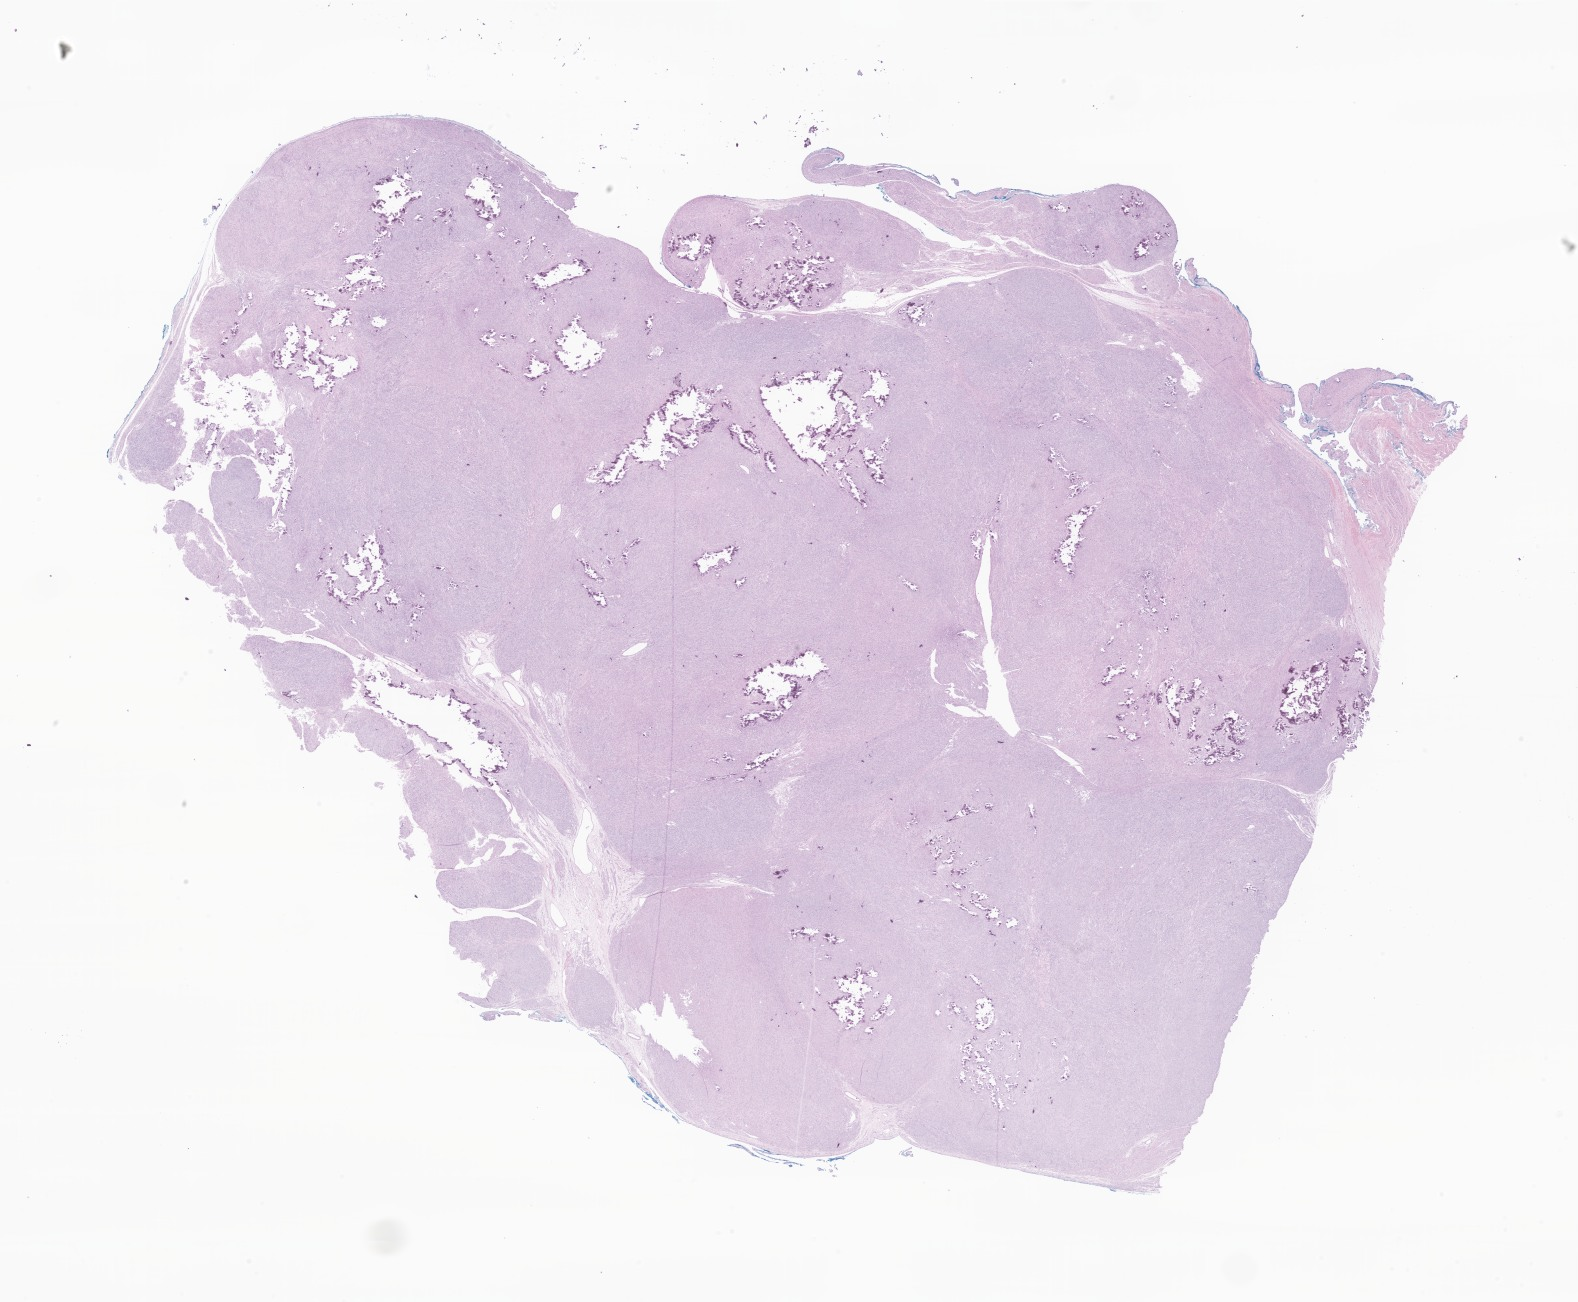
H&E whole-slide image of tumor tissue from the soft tissue of upper extremity — shown as a low-resolution overview of the whole scanned area (about 26.6 x 22.0 mm), FFPE section. Patient male; age 75 months.
Diagnosis: Leiomyosarcoma, NOS.